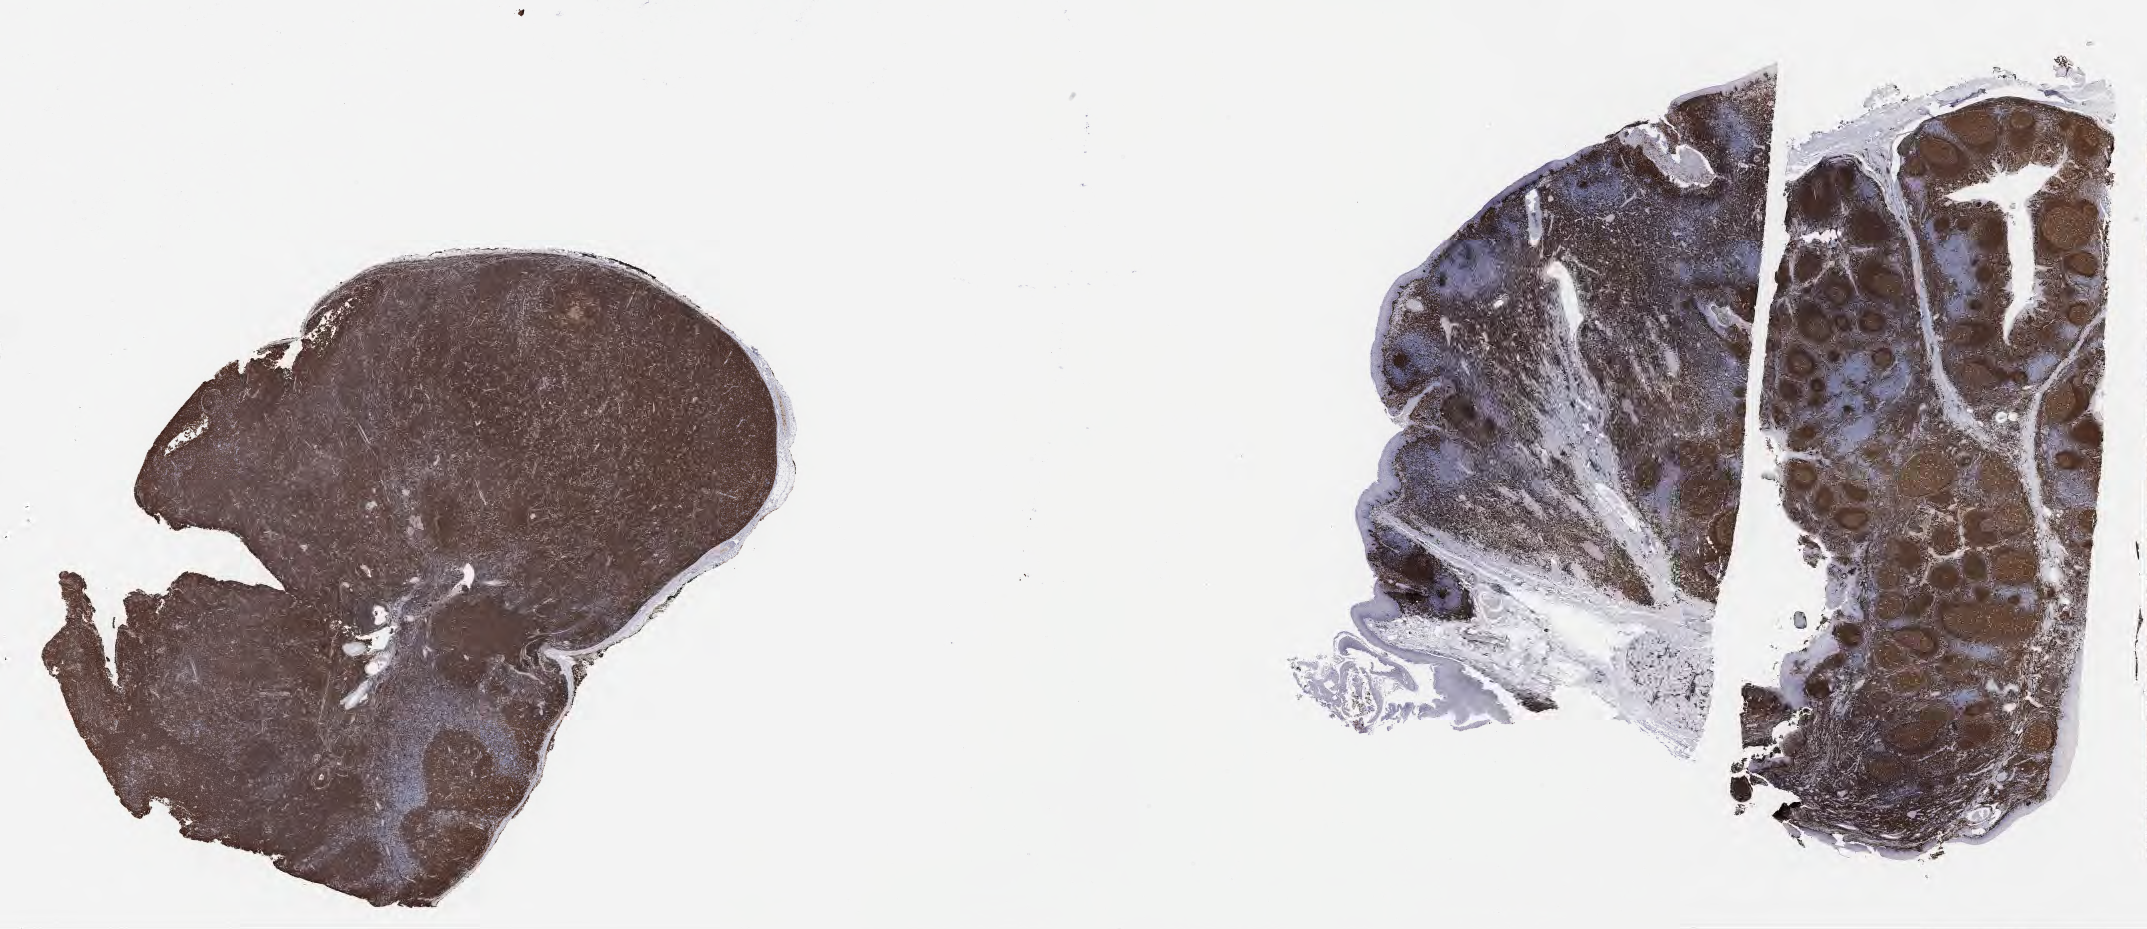
Whole-slide image, immunohistochemical stain for CD79a — whole scanned area (about 34.7 x 15.0 mm) shown as a low-resolution overview, specimen: tumor tissue, anatomic site: lymph node. Patient: male, age 32 years.
Diagnosis: Diffuse large B-cell lymphoma, NOS.